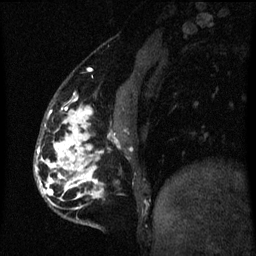
Breast MRI (dynamic contrast-enhanced), one sagittal slice. Slice 18 of 60 in the series (ordered by position). Dynamic contrast-enhanced series, image 2 of 3 at this slice position (ordered by acquisition). 1.5 T. TE 4.2 ms, TR 8 ms. 2 mm slice thickness. 256 × 256 image matrix, field of view 190 × 190 mm. Patient: female, 50 years.
Annotated regions visible in this slice (semi-automatically segmented with operator editing):
- analysis volume of interest (the breast-tissue region the enhancement analysis was run in; not a lesion): bounding box <36,108,118,225> (left, top, right, bottom; pixels)
- tumour enhancement mask (voxels above the 70 % enhancement threshold inside the analysis volume of interest): <36,108,97,199>